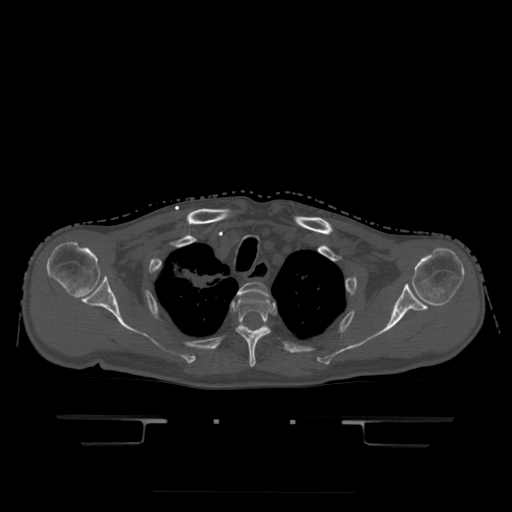
CT including the spine, one axial slice; position 371 of 522 along the scan axis; bone window (W 1800 / L 400 HU); 1.25 mm slice thickness; 512 × 512 image matrix, field of view 436 × 436 mm. Patient age 68 years. From the clinical record (not read from this slice): primary cancer: urothelial.
Outlined on this slice (semi-automatically segmented with operator editing):
- T2 vertebra: bounding box [x1, y1, x2, y2] px = [237, 282, 269, 298]
- T3 vertebra: [236, 292, 273, 367]